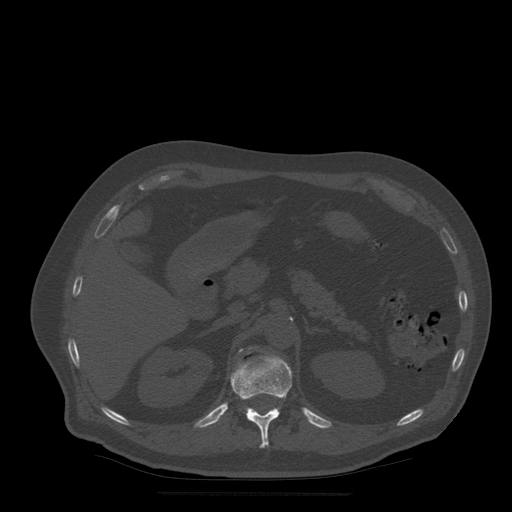
CT including the spine, one axial slice. Slice 215 of 522 in the series (ordered by position). Bone window (W 1800 / L 400 HU). 1.25 mm slice thickness. 512 × 512 image matrix, field of view 420 × 420 mm. Patient age 72 years. Case-level facts recorded for this patient, not image findings: primary cancer: prostate.
Outlined on this slice (semi-automatic segmentation, software-assisted and operator-edited):
- L1 vertebra: bounding box (x1, y1, x2, y2) in pixels: (240, 349, 243, 352)
- T12 vertebra: (231, 356, 292, 449)